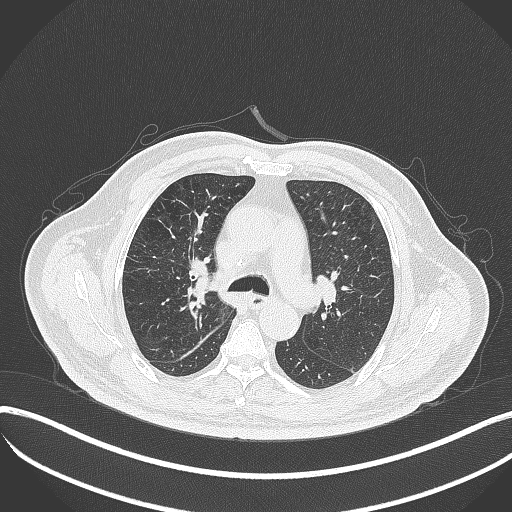
Chest CT, one axial slice; slice 240 of 401 in the series (ordered by position); lung window (W 1500 / L -600 HU); 512 × 512 image matrix, field of view 400 × 400 mm. Patient: male, 72 years. Case-level facts recorded for this patient, not image findings: clinical TNM (as recorded): T1c N0 M0; histopathological grade: G2.
Structures marked on this image (bounding box drawn by a radiologist):
- lung tumour (recorded histology: squamous cell carcinoma): bounding box (x1, y1, x2, y2) in pixels: (183, 263, 215, 306)